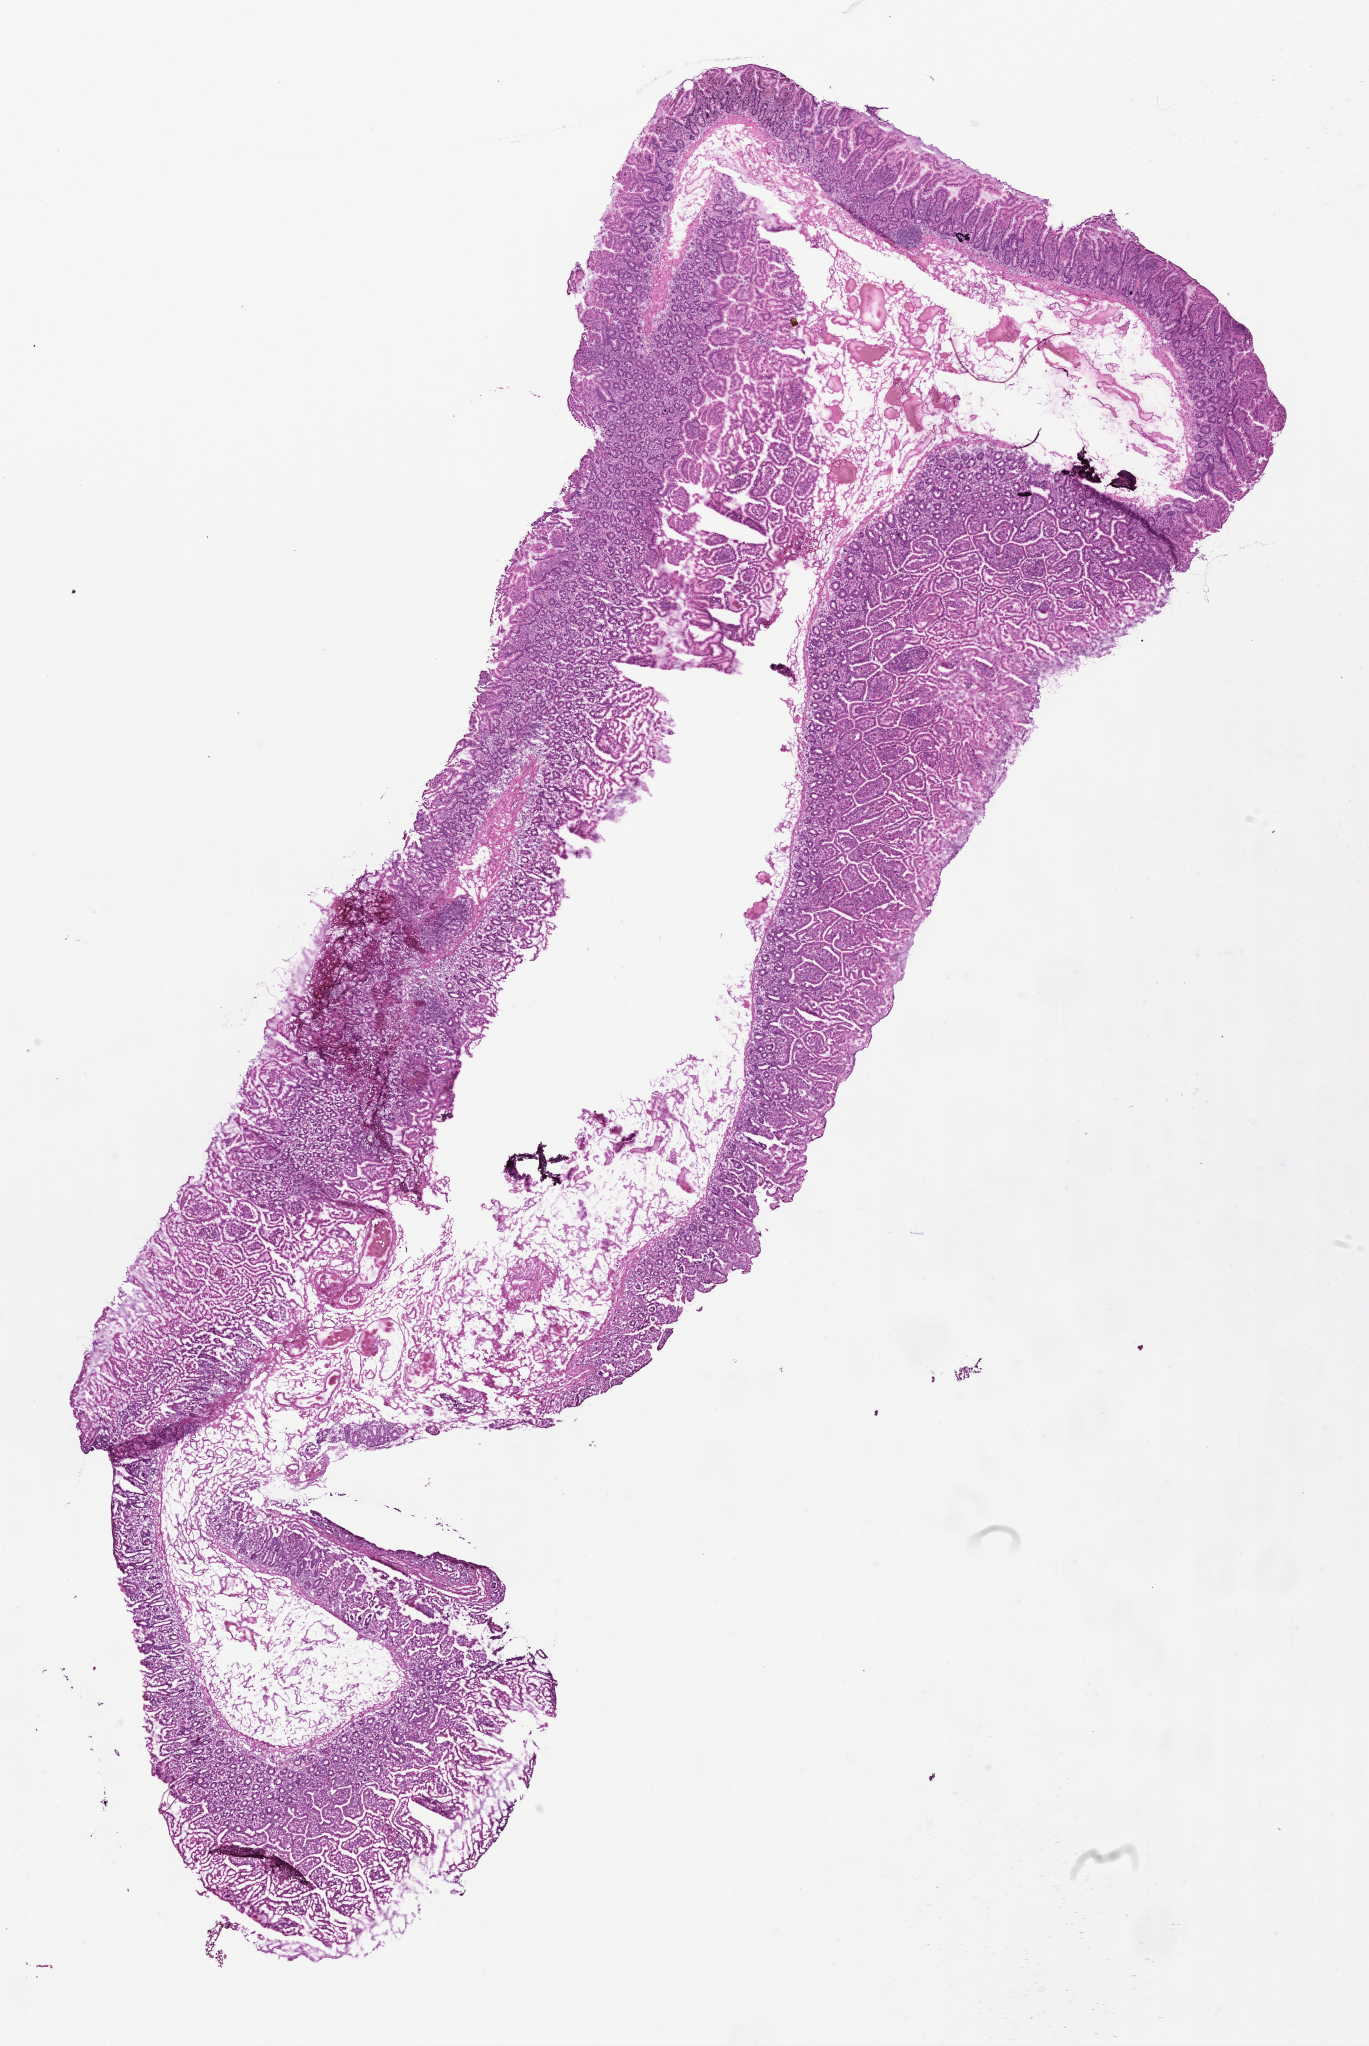
Haematoxylin and eosin whole-slide image, a low-resolution overview of the entire scanned area, about 11.1 x 16.6 mm, cryosection, specimen: non-tumor (normal tissue) sample from a patient with cholangiocarcinoma. Male patient; age at initial diagnosis 73 years. Pathologist review of this section (percent, as recorded): tumor cells 0%, tumor nuclei 0%, stromal cells 0%, necrosis 0%, normal cells 100%. Inflammatory infiltration, as recorded: lymphocyte infiltration 15%, monocyte infiltration 2%, neutrophil infiltration 10%.
• this section: non-tumor tissue sample; the patient's diagnosis is given above
• section: bottom of the tissue portion